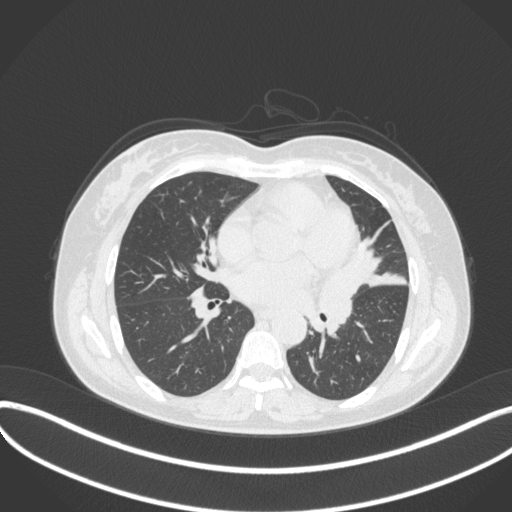
Chest CT, one axial slice. Reconstruction kernel B31f. 120 kVp. Lung window (W 1500 / L -600 HU). 1 mm slice thickness. 512 × 512 image matrix. Patient: female, 54 years. Case-level facts recorded for this patient, not image findings: clinical TNM (as recorded): T2a N1 M0.
Structures marked on this image (bounding box drawn by a radiologist):
- lung tumour (recorded histology: small cell carcinoma): box from (x=318, y=272) to (x=361, y=332) px